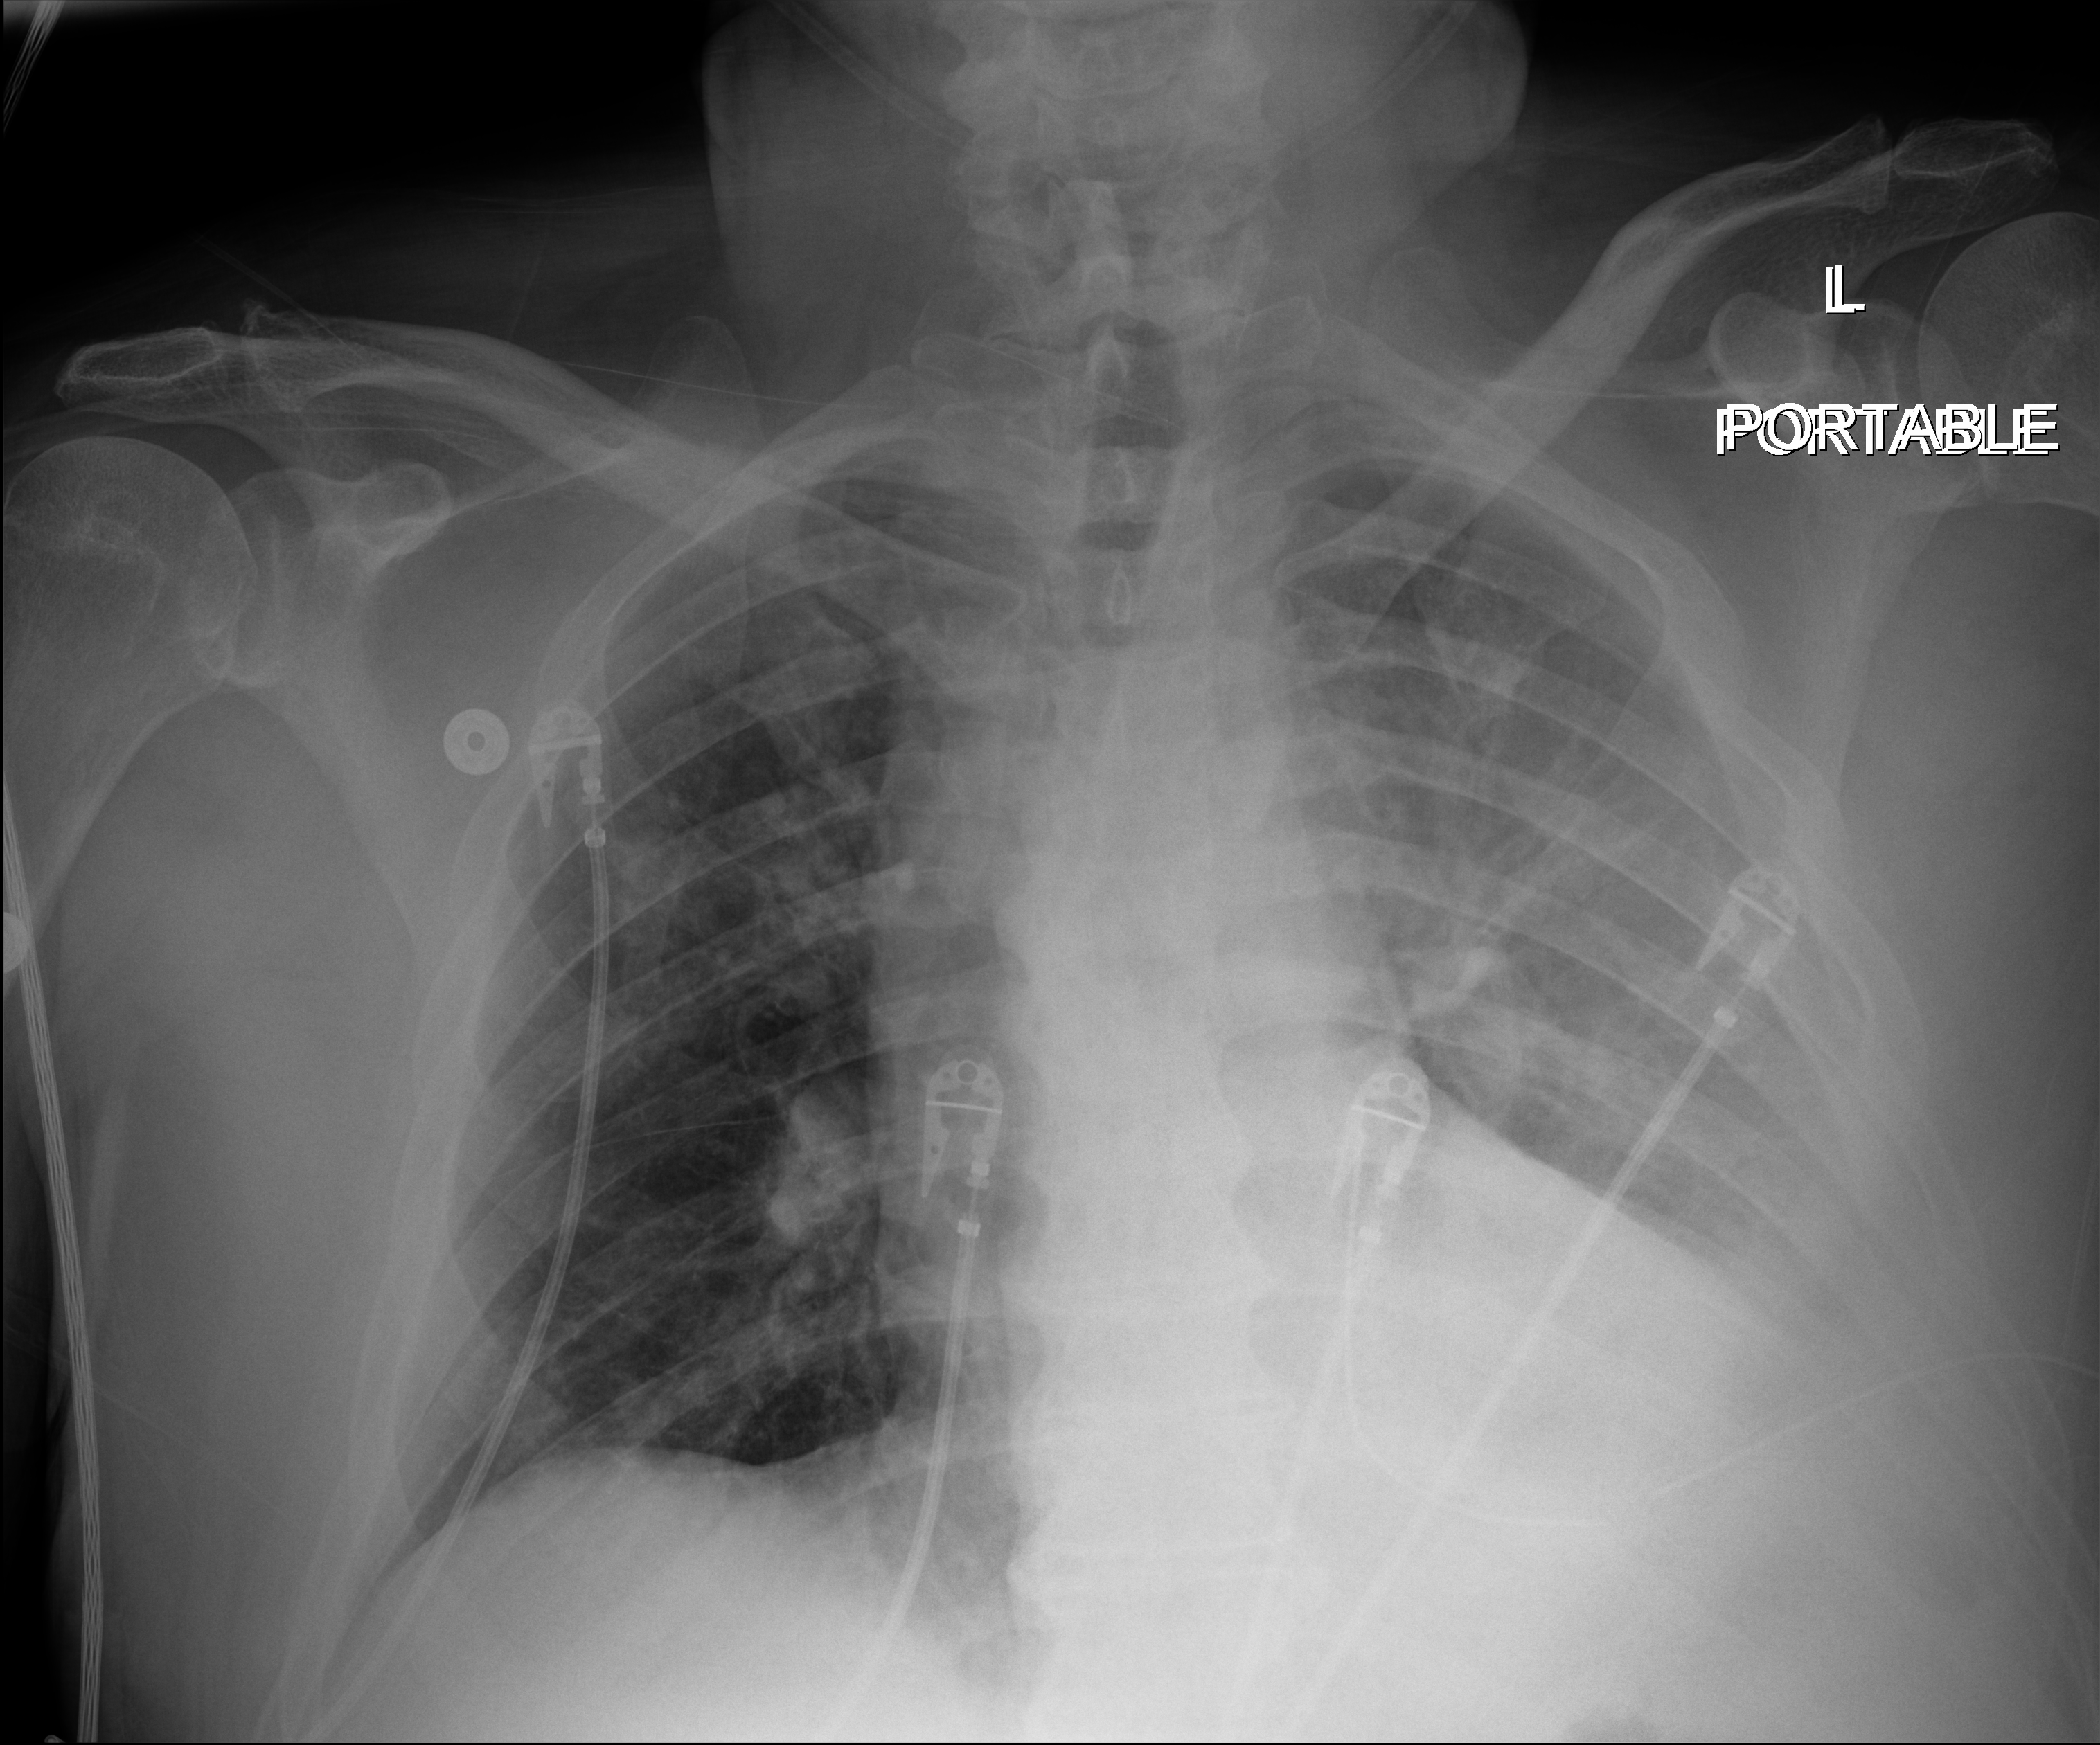
Chest X-ray (portable), anteroposterior (AP) projection. Male patient hospitalised with COVID-19, age 18–59 years.
Admission-level facts for this patient (not findings on this image; timing relative to this image not recorded): admitted to intensive care during this hospital stay: no.